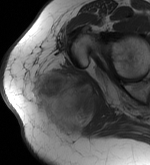
MRI of an extremity soft-tissue mass, one axial slice; position 38 of 56 along the scan axis; MR volume resampled by the dataset authors to the PET/CT grid (not the native acquisition matrix); 150 × 165 image matrix, field of view 146 × 161 mm. Female patient. From the clinical record (not read from this slice): histological type: epithelioid sarcoma with vascular differentiation; site of the primary tumour: right buttock.
Structures marked on this image (expert contour drawn on MRI and transferred to this co-registered scan by the dataset authors):
- gross tumour volume (mass): bounding box (x1, y1, x2, y2) in pixels: (32, 70, 106, 132)